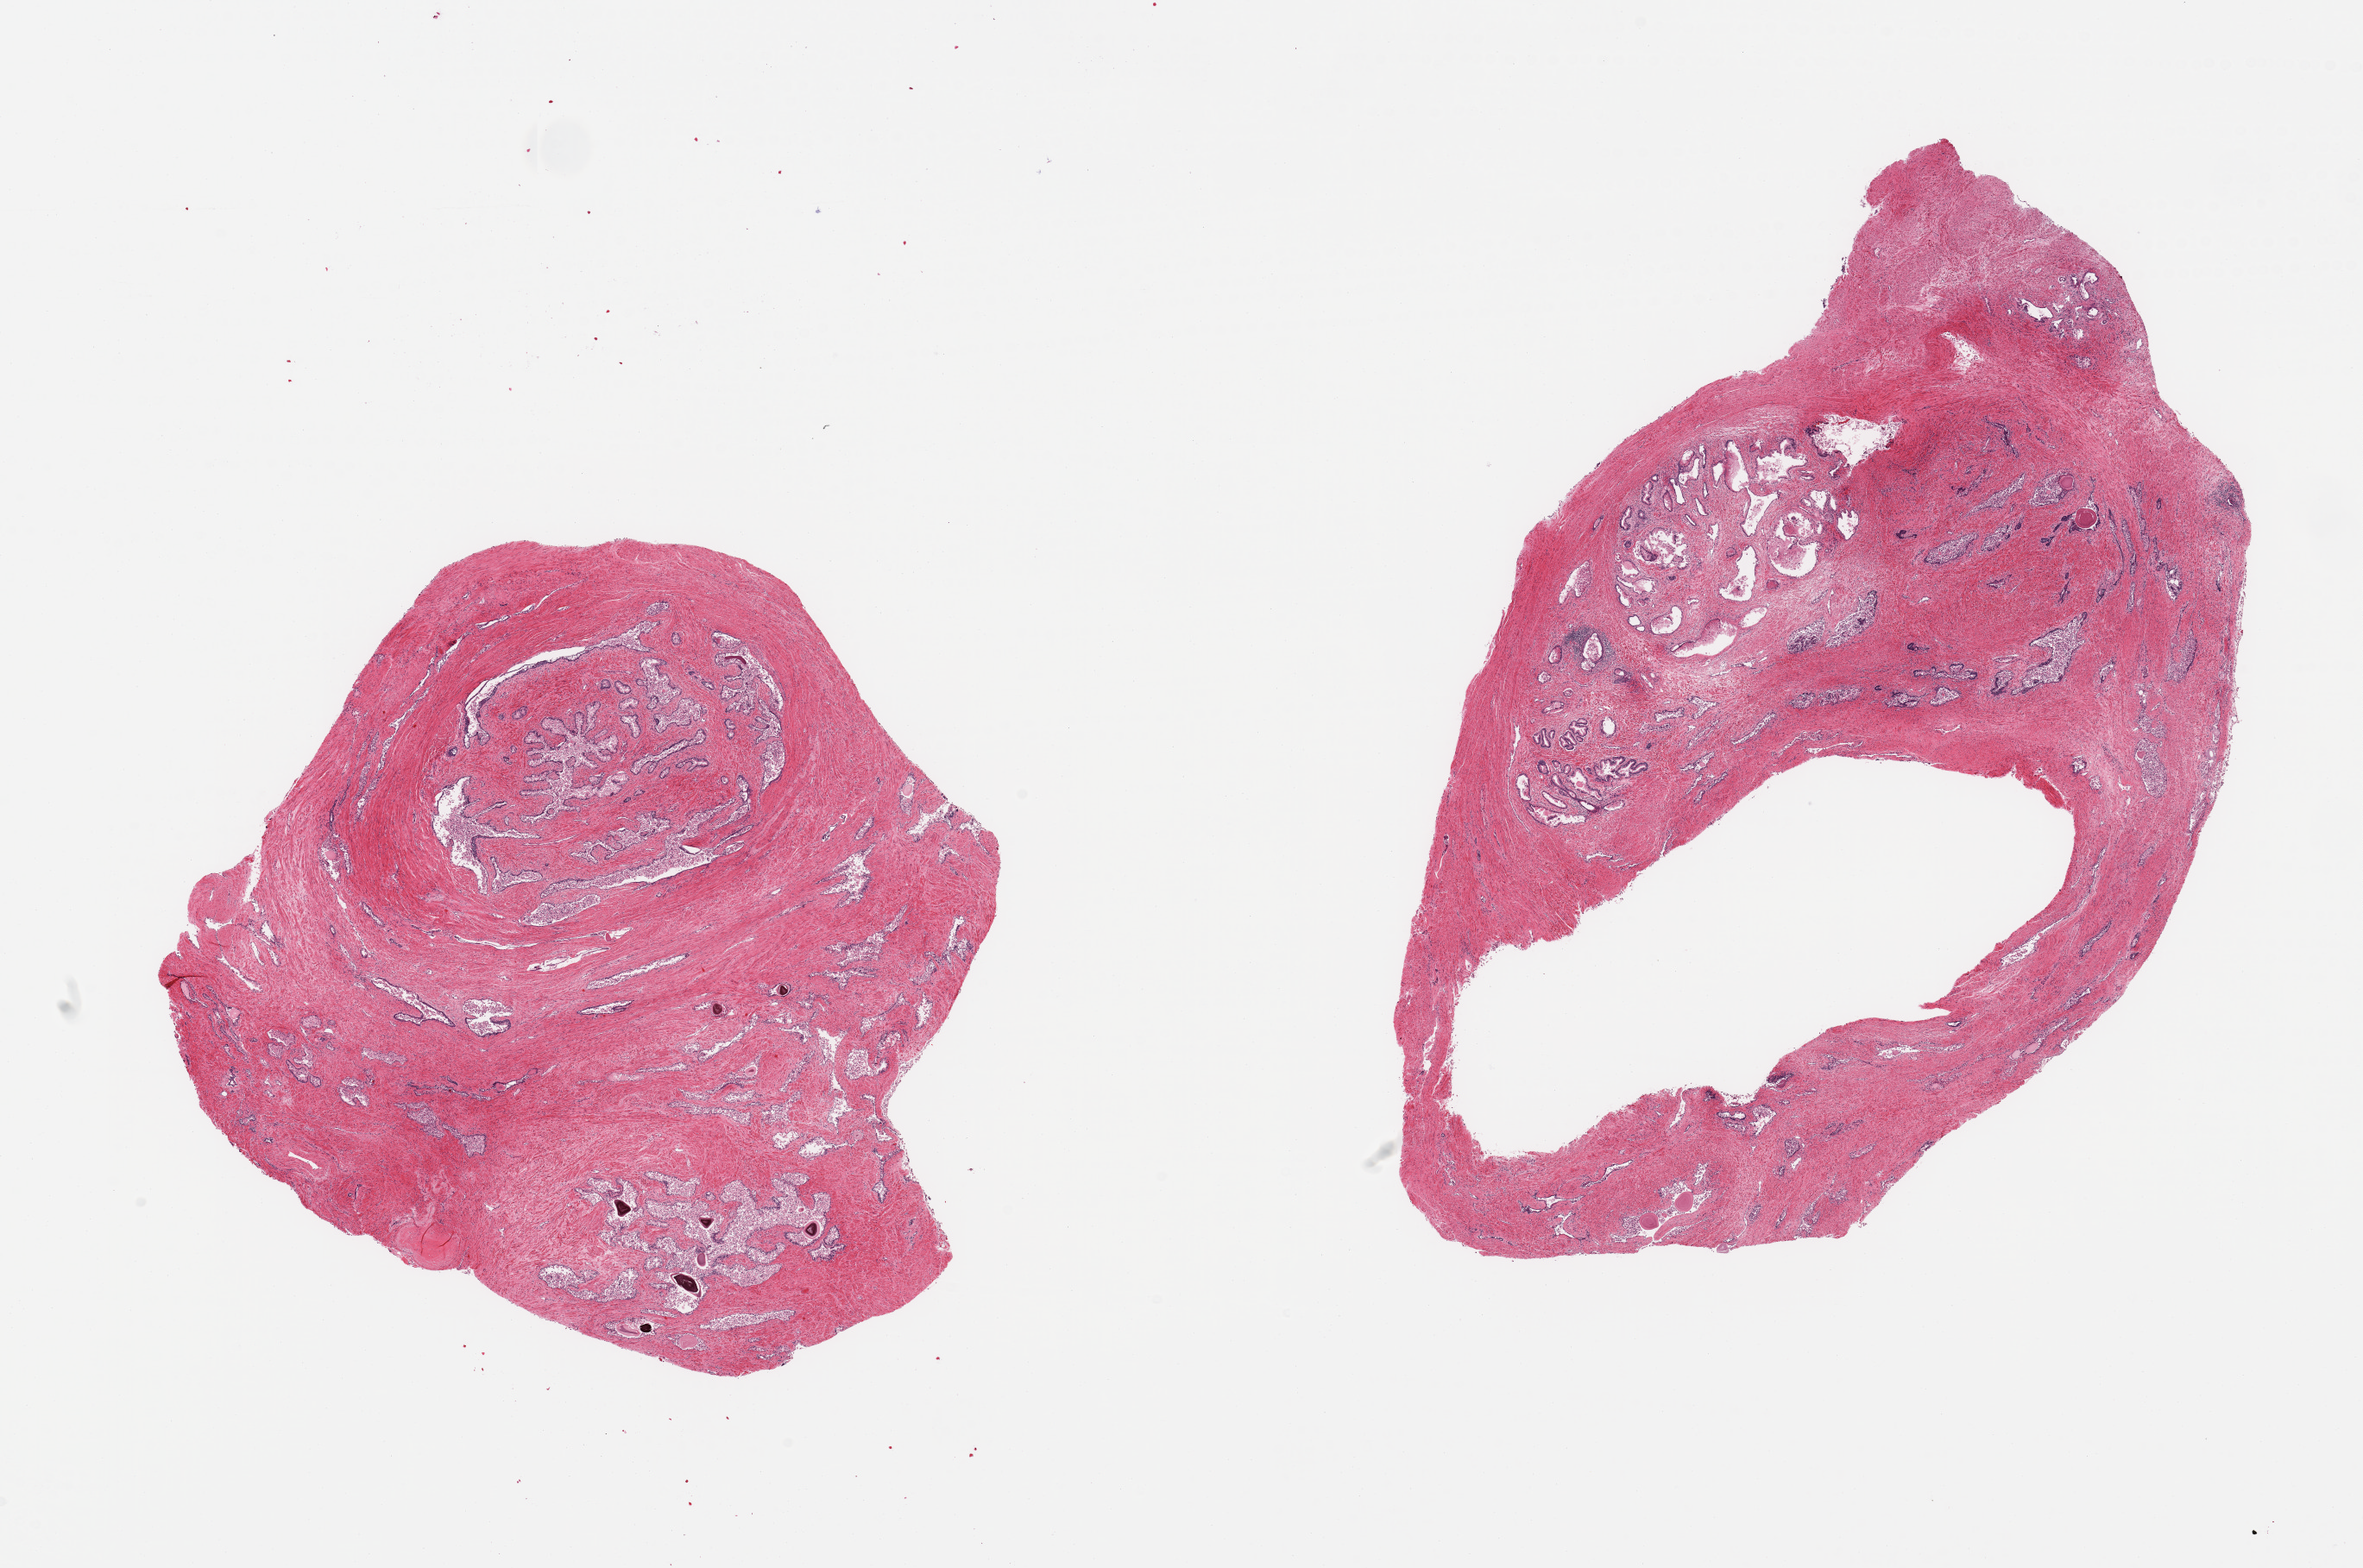
Whole-slide image, hematoxylin and eosin (H&E) stain, brightfield — low-resolution overview of the scanned area, about 21.7 x 14.4 mm (from a 20x scan). PAXgene-fixed, paraffin-embedded tissue. Sampled site (target tissue): prostate. Donor tissue sample. Donor: male.
* review note (as recorded): 2 pieces, glandular elements with advanced autolysis; pronounced nodular glandular and stromal htyprerplasia